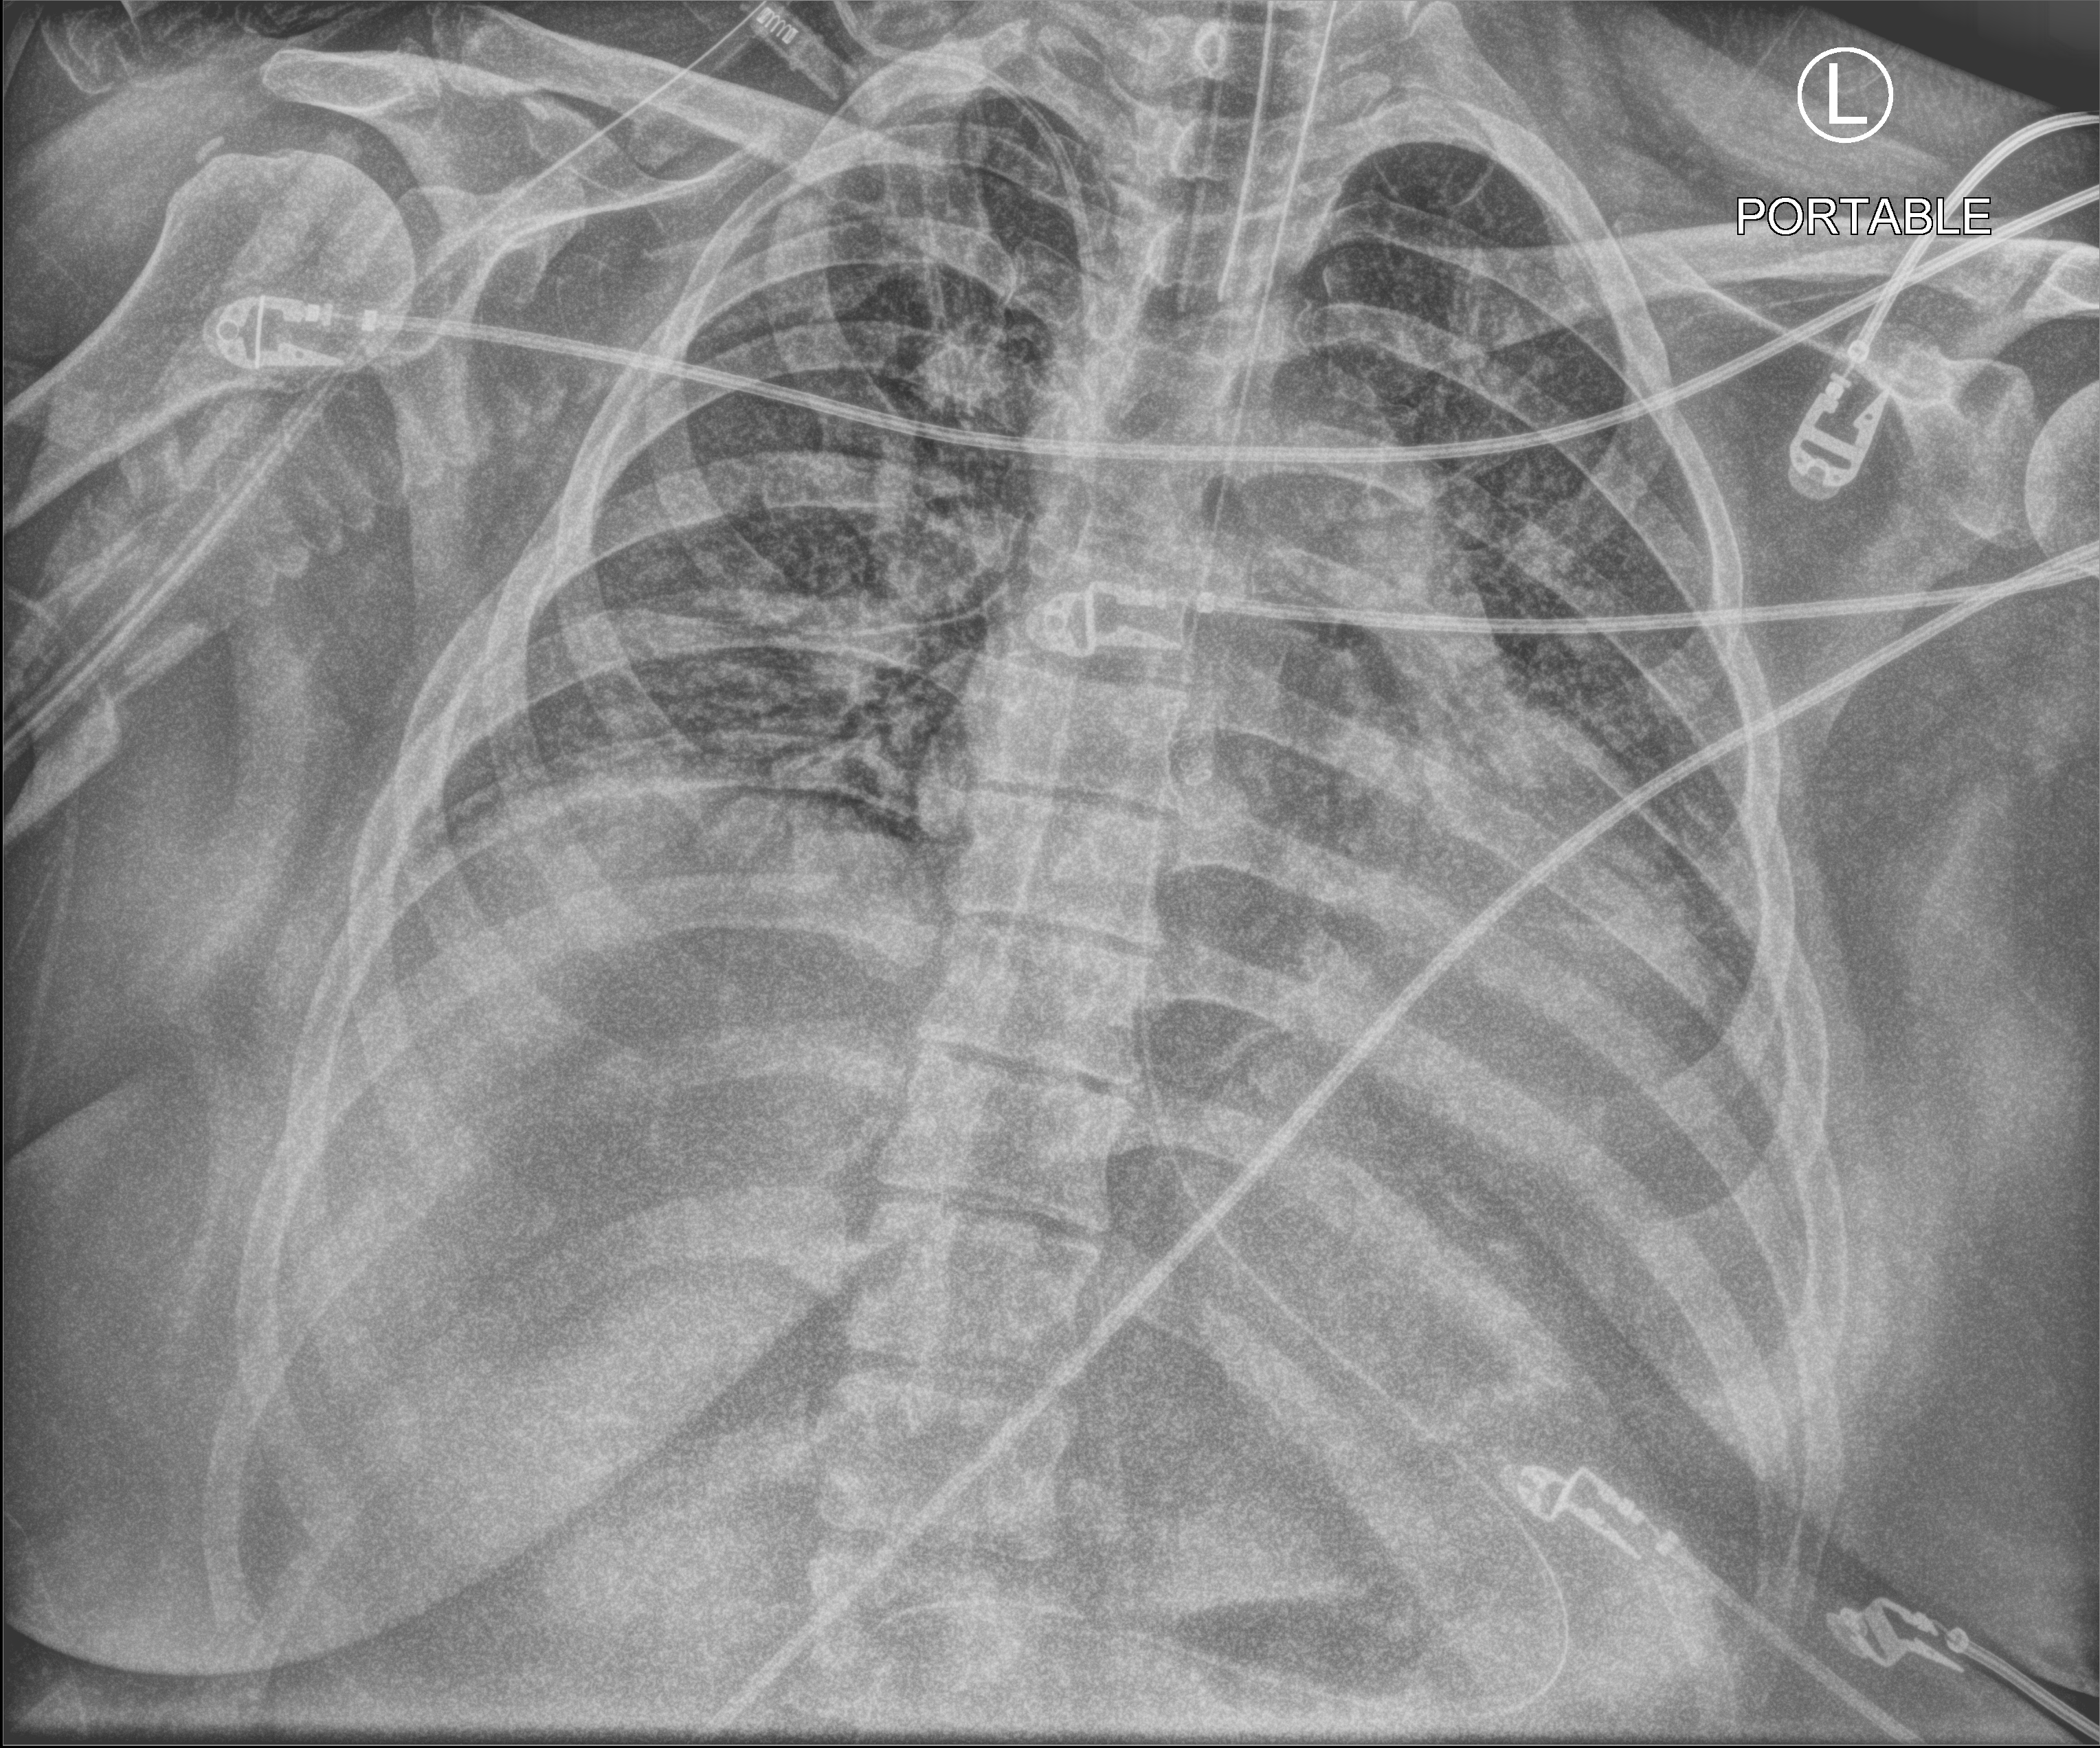
Chest X-ray (portable), anteroposterior (AP) projection. Female patient hospitalised with COVID-19, age 18–59 years.
Admission-level facts for this patient (not findings on this image; timing relative to this image not recorded):
- admitted to intensive care during this hospital stay: yes
- mechanically ventilated during this hospital stay: yes